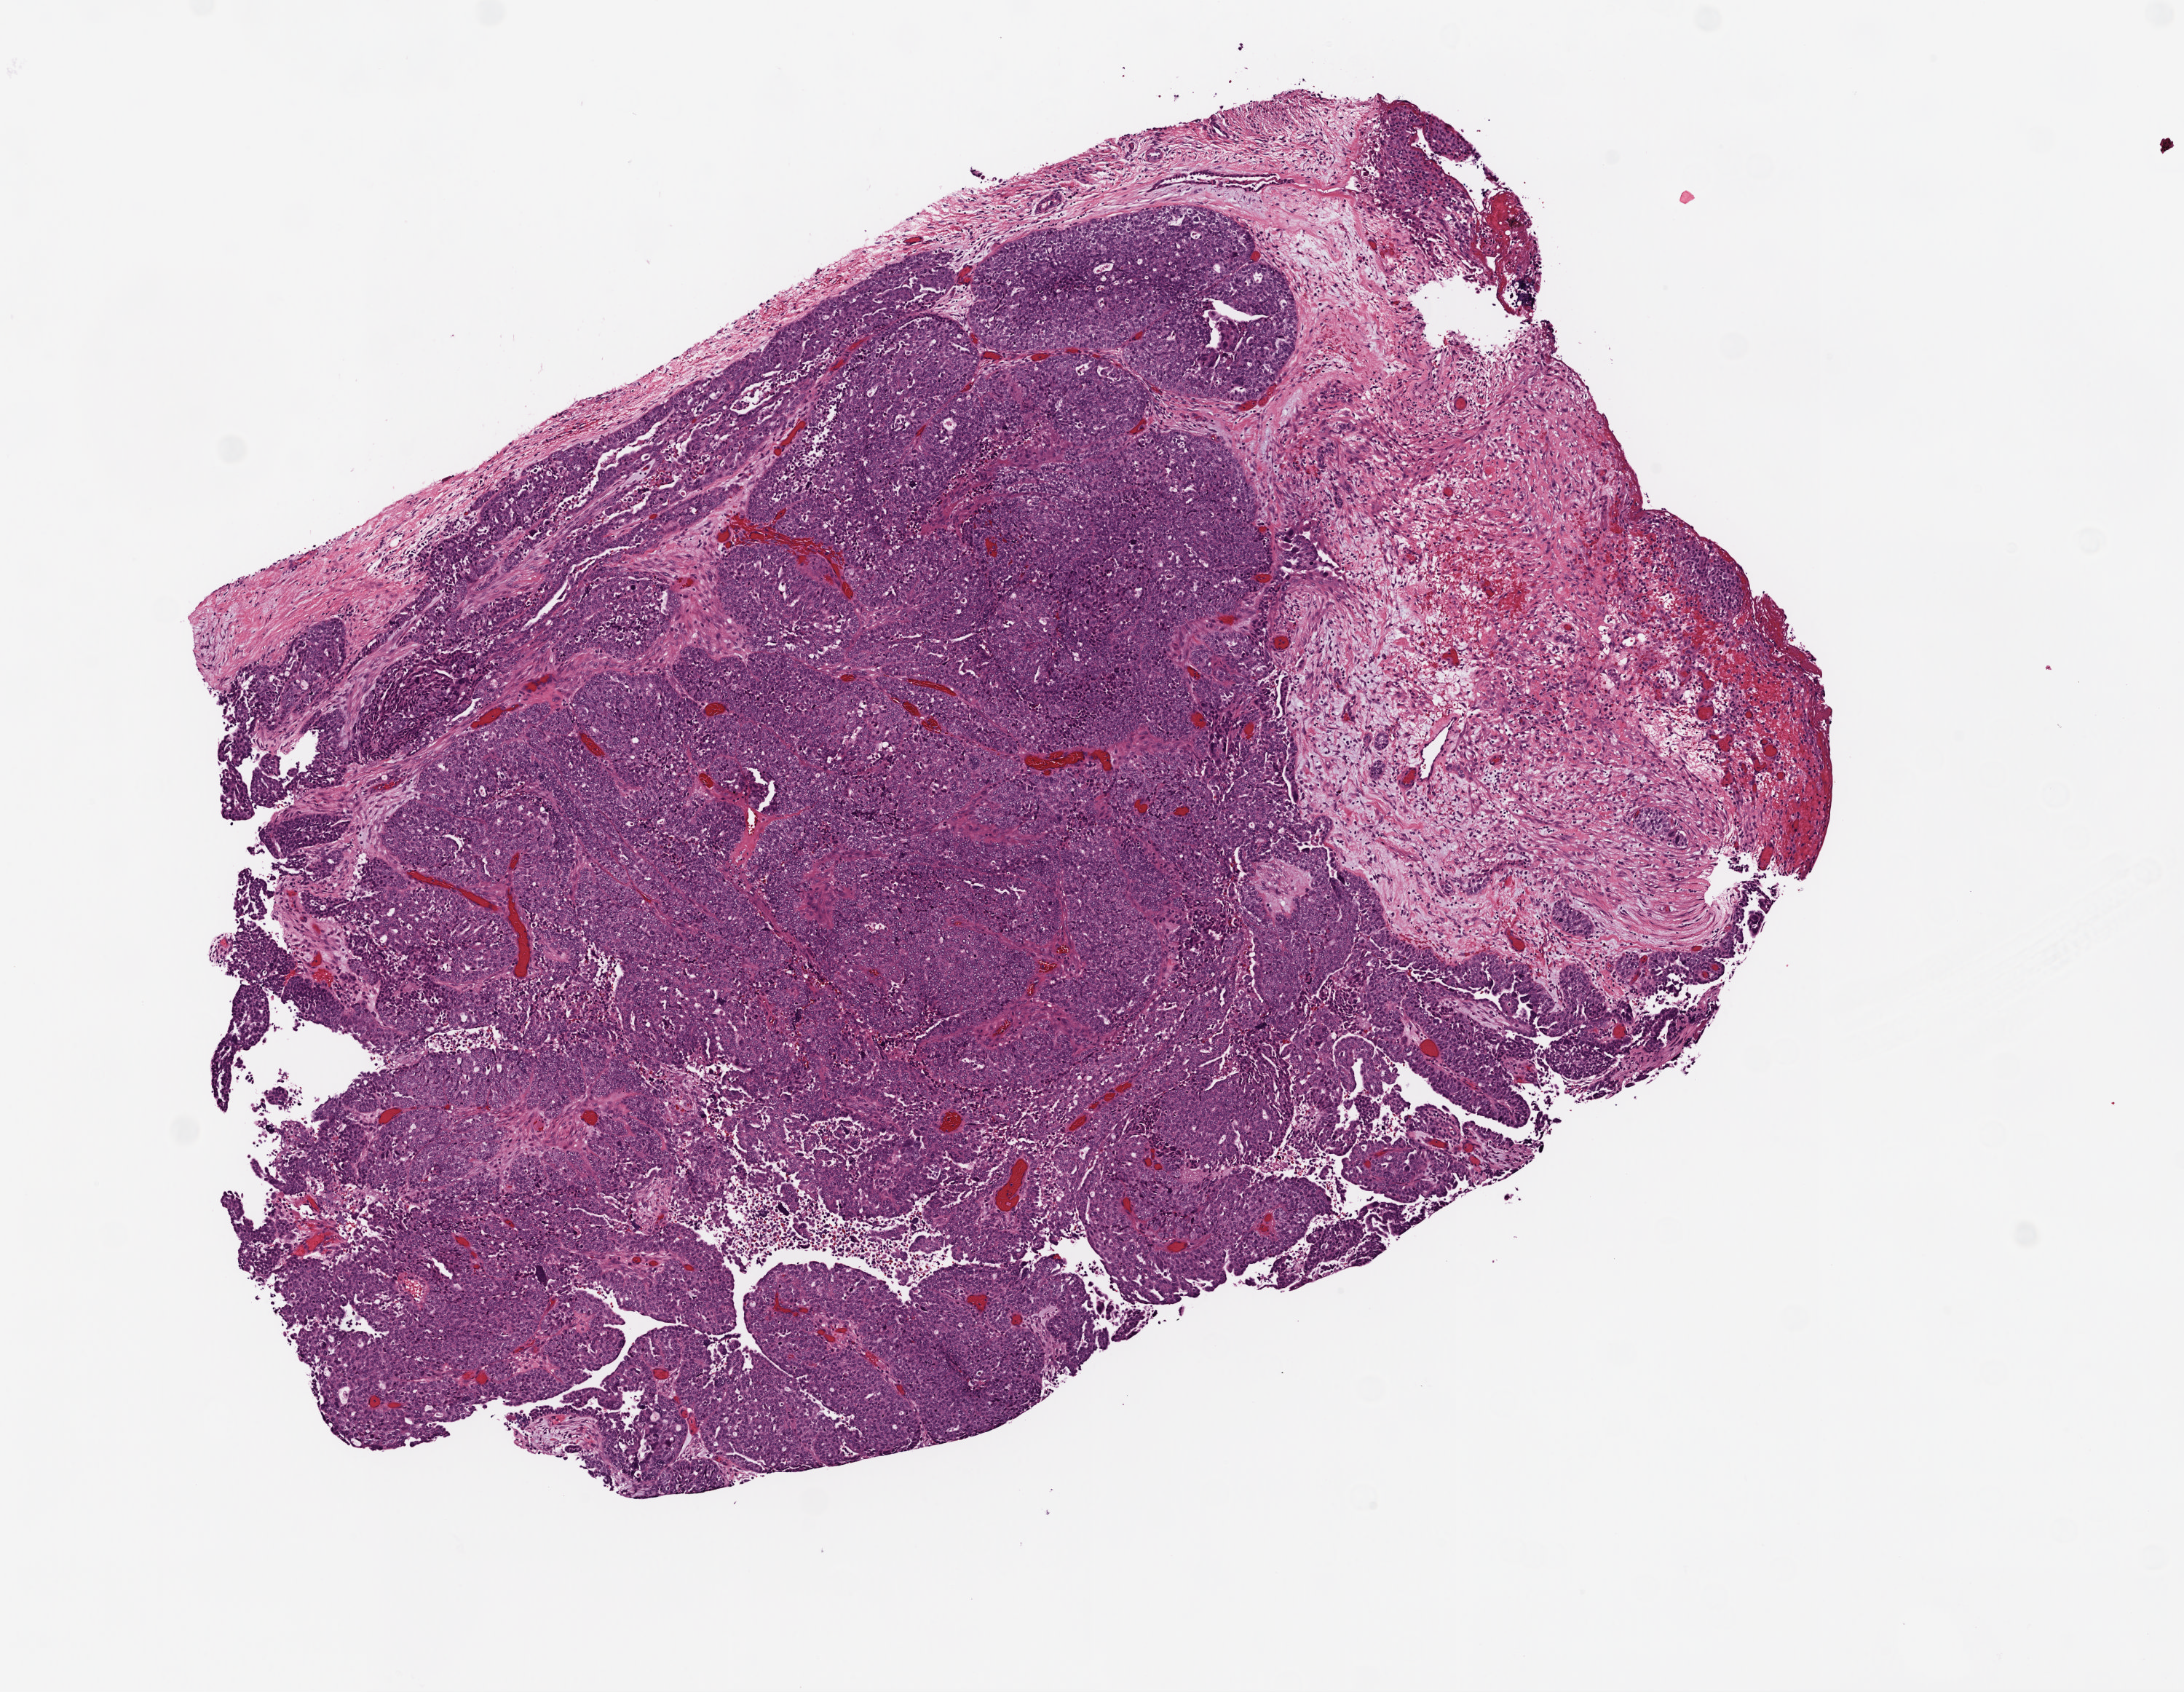
Whole-slide histology image, H&E-stained, low-resolution overview of the scanned area, about 6.0 x 4.7 mm (acquisition: 20x scan). Frozen section. Primary tumour sample from the ovary. Patient: female, age at initial diagnosis 54 years. Histologic grade: G3 (poorly differentiated). Slide review estimates, as recorded: tumour cells 74%, tumour nuclei 90%, normal cells 0%, stromal cells 25%, necrosis 1%.
• laterality: bilateral
• FIGO stage: IIIC
• histologic diagnosis: Serous cystadenocarcinoma, NOS